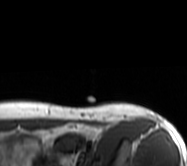
MRI of an extremity soft-tissue mass, one axial slice; slice 51 of 62 in the series (ordered by position); MR volume resampled by the dataset authors to the PET/CT grid (not the native acquisition matrix); 3.27 mm slice thickness; 187 × 166 image matrix, field of view 183 × 162 mm. Female patient. From the clinical record (not read from this slice): histological type: leiomyosarcoma; grade: high; site of the primary tumour: groin.
Structures marked on this image (expert contour drawn on MRI and transferred to this co-registered scan by the dataset authors):
- gross tumour volume including surrounding oedema: bounding box (x1, y1, x2, y2) in pixels: (89, 103, 156, 123)